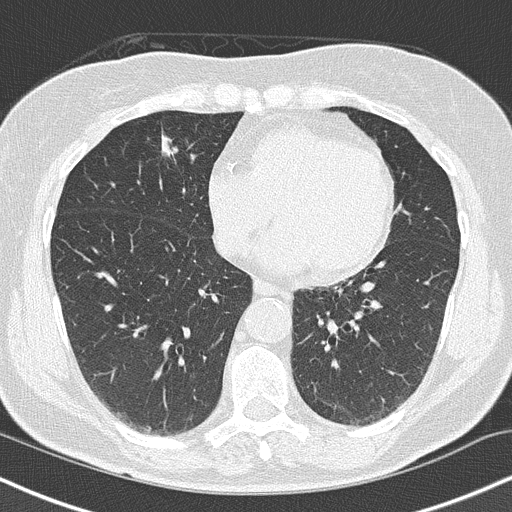
Low-dose screening chest CT, axial slice, first (baseline) screen, lung window (W 1500 / L -600 HU), lung (sharp) reconstruction kernel (B50f), slice 89 of 145 in the series, 512 × 512 image matrix. Female participant, aged 66 years at enrolment. Current smoker at enrolment.
• Expert-annotated lung lesion, bounding box <144,127,184,166> (left, top, right, bottom; pixels).
• Reader record for this screening exam (exam-level; its link to the box is not recorded): non-calcified nodule or mass ≥4 mm, right lower lobe, 10 × 8 mm, smooth margins, soft tissue attenuation.
• Official screen result: positive, change unspecified: nodule(s) >= 4 mm or enlarging nodule(s), mass(es), or other non-specific abnormalities suspicious for lung cancer.